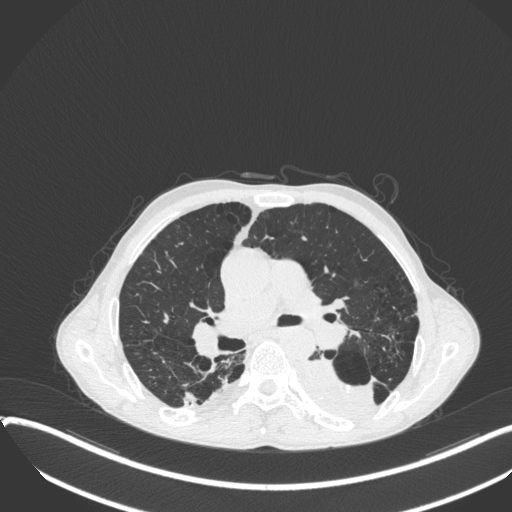
Chest CT, one axial slice. Slice 227 of 400 in the series (ordered by position). 120 kVp. Lung window (W 1500 / L -600 HU). 1 mm slice thickness. 512 × 512 image matrix. Male patient, age 57 years. Case-level facts recorded for this patient, not image findings: clinical TNM (as recorded): T4 N0 M0.
Structures marked on this image (bounding box drawn by a radiologist):
- lung tumour (recorded histology: squamous cell carcinoma): bounding box (x1, y1, x2, y2) in pixels: (294, 350, 379, 425)